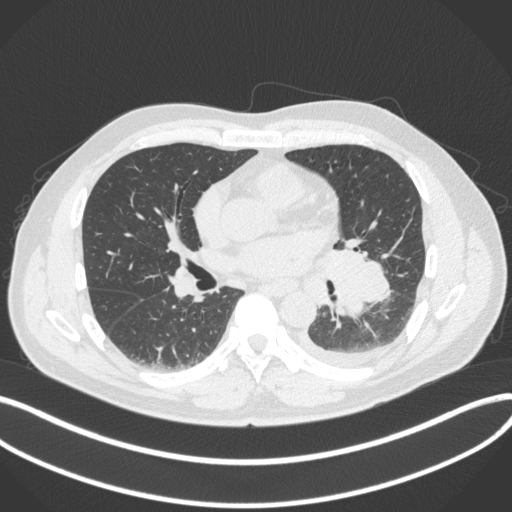
Chest CT, one axial slice. Slice 182 of 350 in the series (ordered by position). Reconstruction kernel B31f. Lung window (W 1500 / L -600 HU). 1 mm slice thickness. 512 × 512 image matrix, field of view 400 × 400 mm. Male patient, age 58 years. Case-level facts recorded for this patient, not image findings: clinical TNM (as recorded): T3 N1 M1b; histopathological grade: G3.
Annotated regions visible in this slice (bounding box drawn by a radiologist):
- lung tumour (recorded histology: small cell carcinoma): box from (x=321, y=239) to (x=393, y=318) px